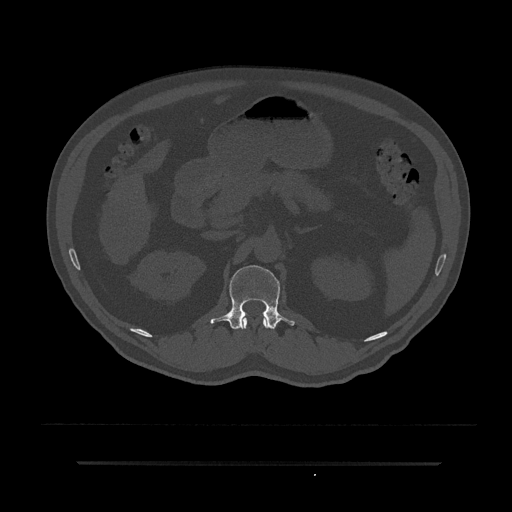
CT including the spine, one axial slice. Position 161 of 797 along the scan axis. 120 kVp. Bone window (W 1800 / L 400 HU). 0.5 mm slice thickness. 512 × 512 image matrix. Male patient, age 59 years. Case-level facts recorded for this patient, not image findings: primary cancer: bile ducts.
Structures marked on this image (semi-automatically segmented with operator editing):
- L1 vertebra: box from (x=210, y=265) to (x=295, y=330) px
- T12 vertebra: (x=241, y=315)–(x=268, y=330)